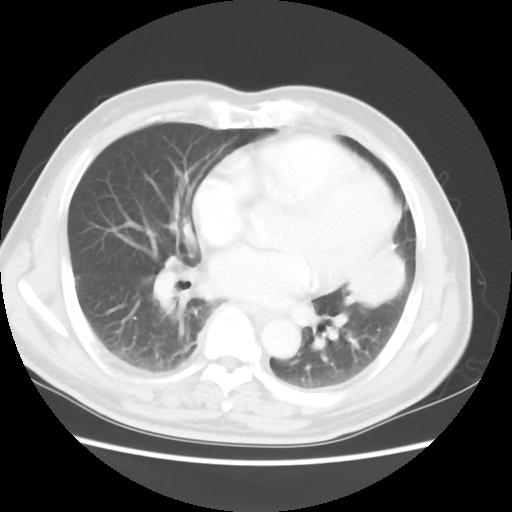
Chest CT, one axial slice; 120 kVp; lung window (W 1500 / L -600 HU); 512 × 512 image matrix, field of view 360 × 360 mm. Male patient, age 69 years. From the clinical record (not read from this slice): clinical TNM (as recorded): T3 N1 M1a.
Structures marked on this image (rectangle marked by the reading radiologist):
- lung tumour (recorded histology: squamous cell carcinoma): bounding box <332,230,414,321> (left, top, right, bottom; pixels)